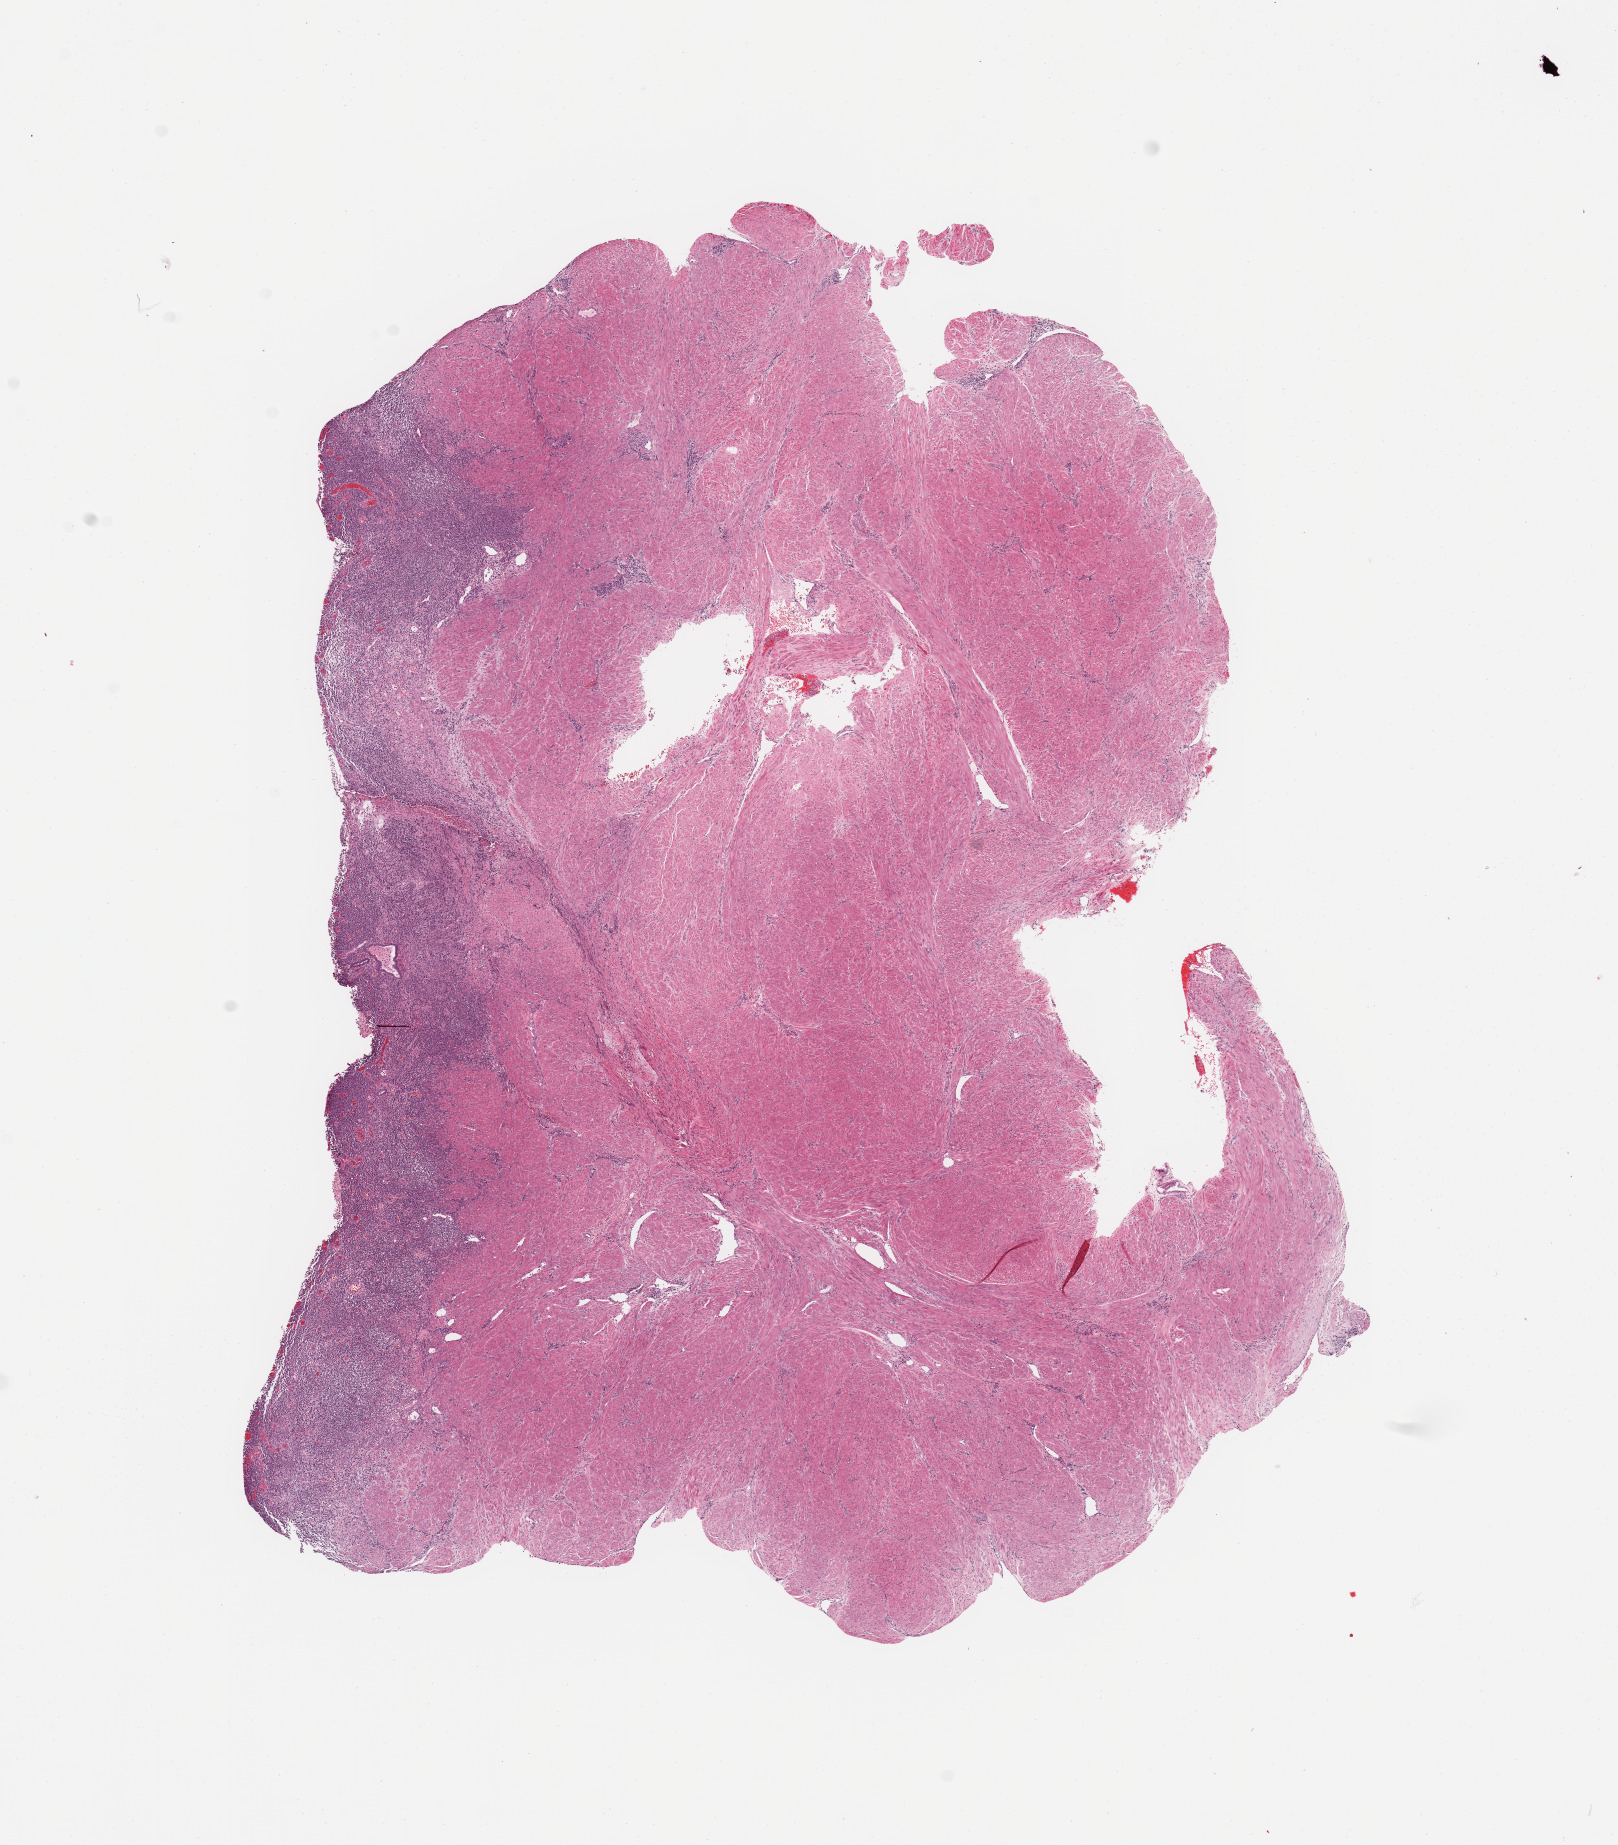
Hematoxylin and eosin (H&E) stained whole-slide image, shown as a low-resolution overview of the whole scanned area (about 12.8 x 14.6 mm). Female, 62 y/o.
Patient diagnosis (cohort enrolment): sarcoma (site not recorded at cohort level). Primary tumour site (as recorded): gynecologic.